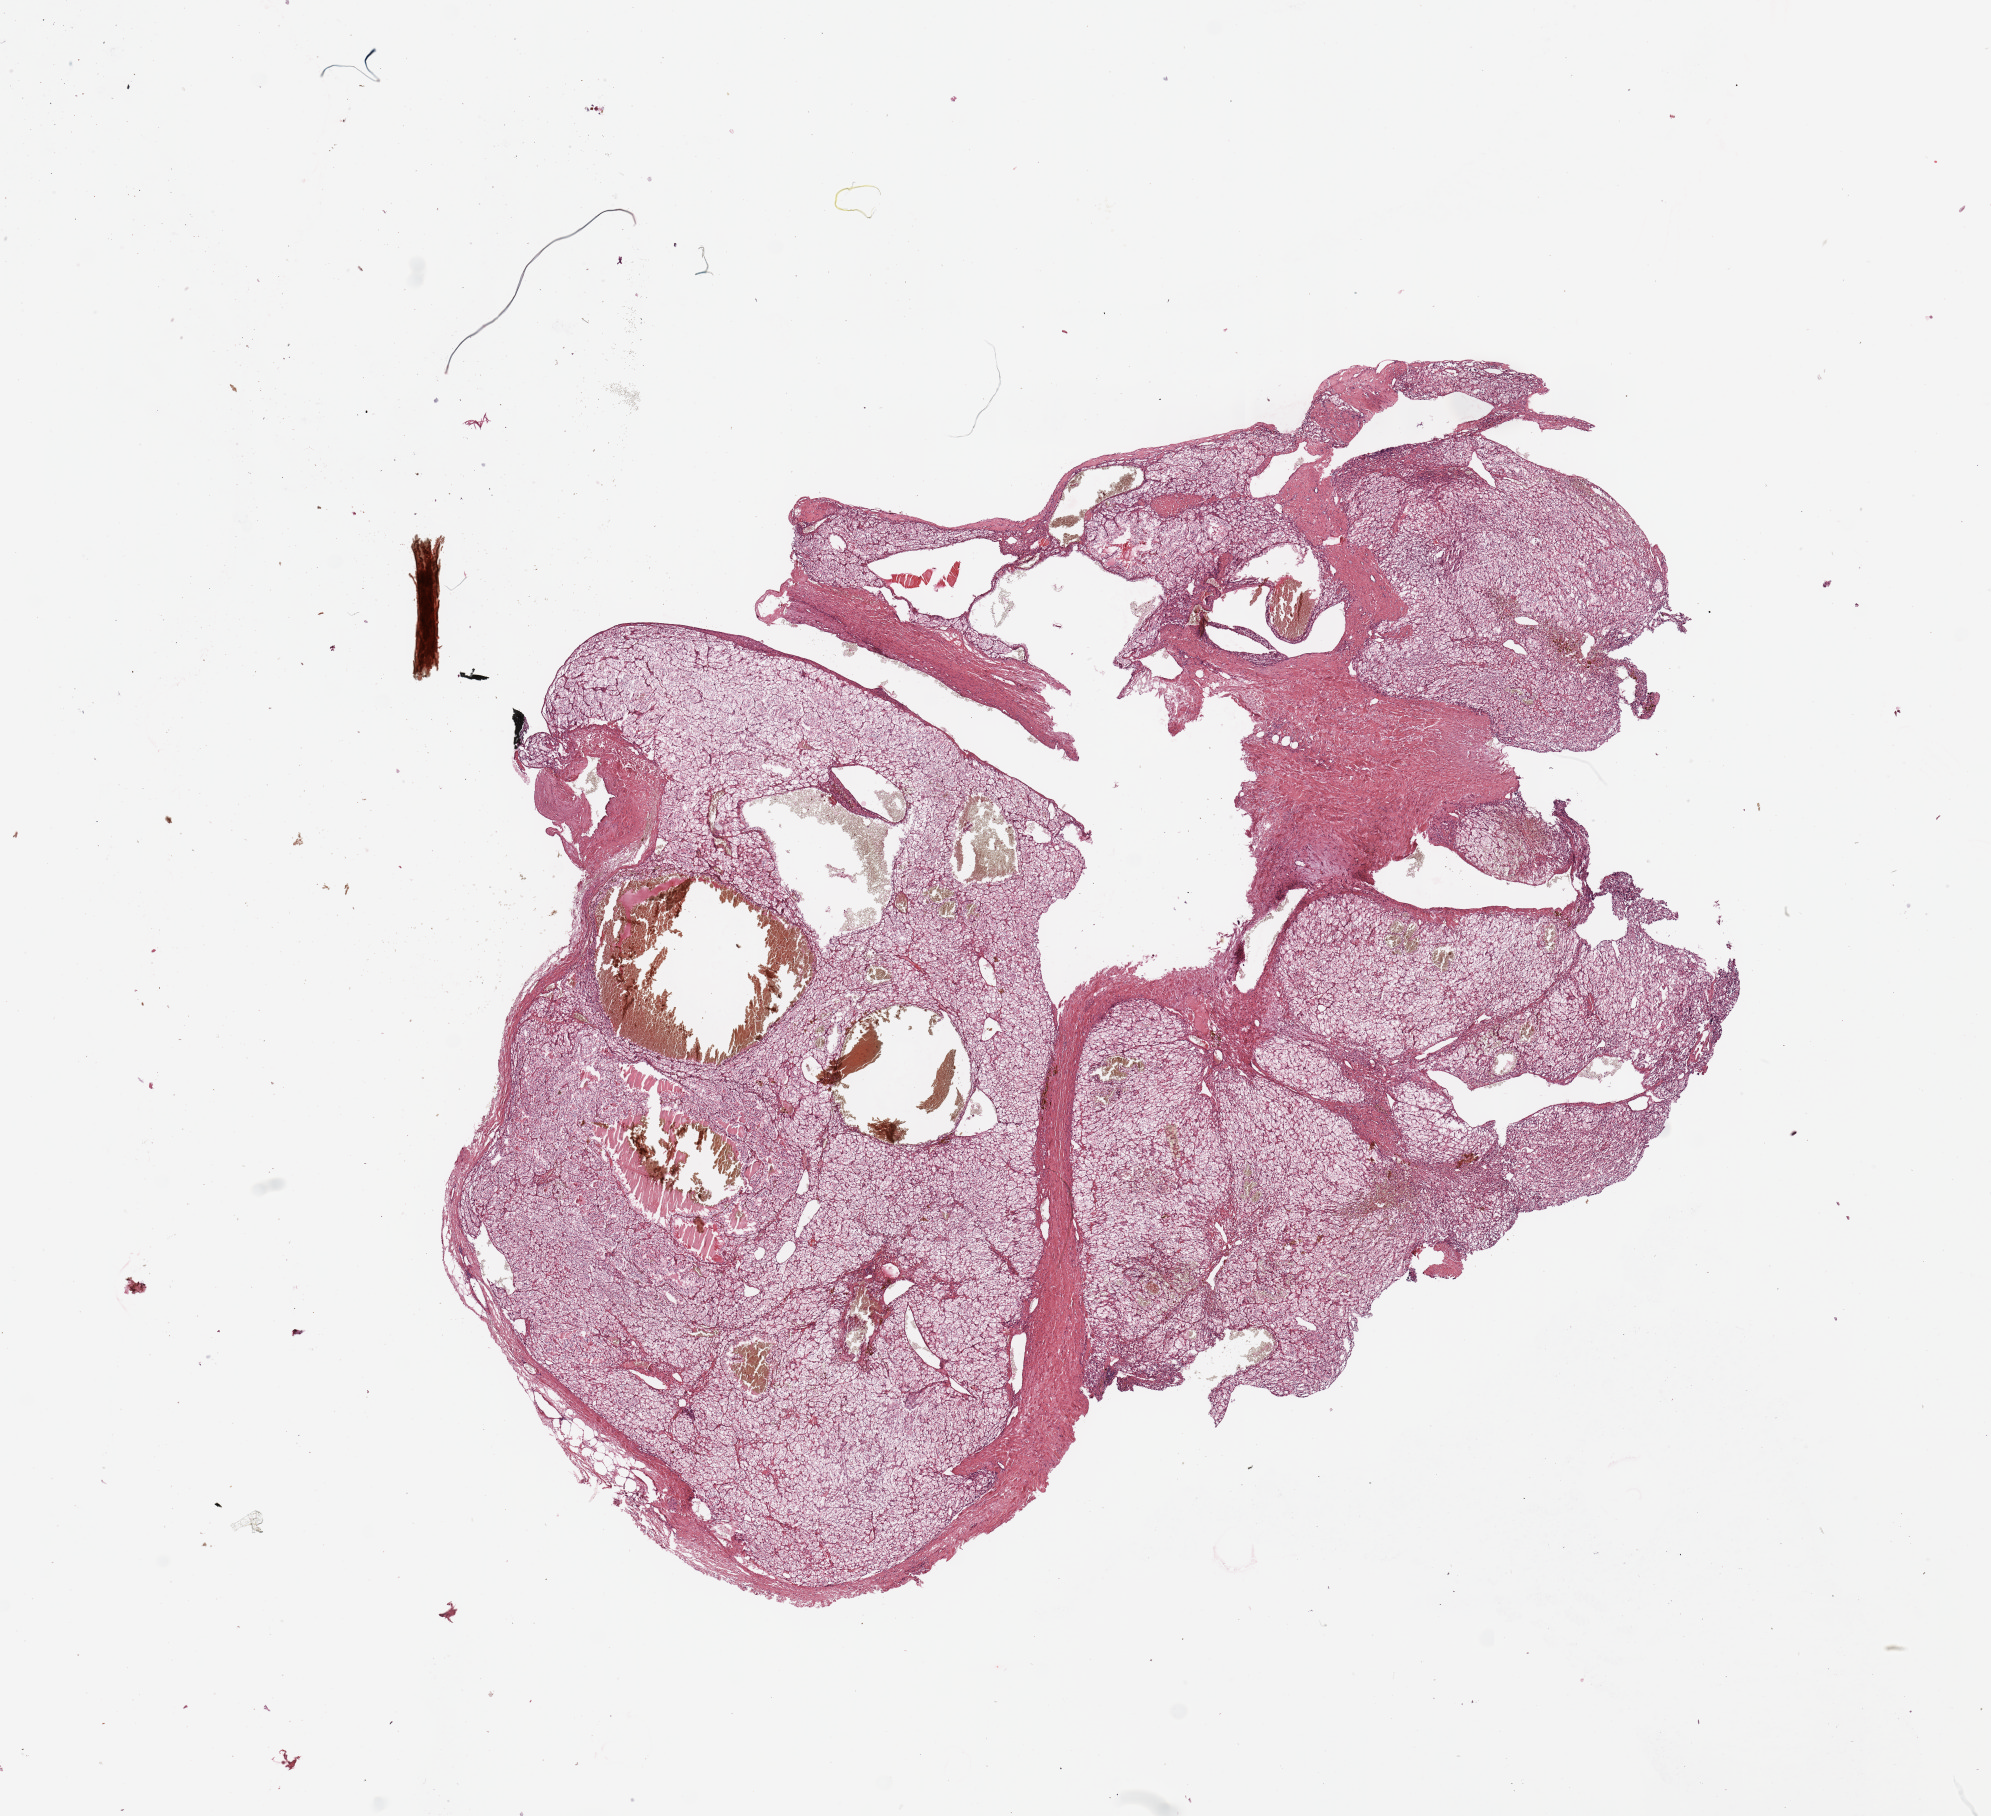
Hematoxylin and eosin (H&E) stained whole-slide image, a low-resolution overview of the entire scanned area, about 15.8 x 14.4 mm (slide scanned at 20x). Tumour tissue sample, sampled site: kidney. Female, 67 y/o. Histologic grade: G2 (moderately differentiated). Pathologist review of this section (percent, as recorded): tumour nuclei 85%, necrosis 2%.
Primary tumour site (as recorded): lower pole. Histologic diagnosis: Renal cell carcinoma, NOS. AJCC pathologic stage: IV.